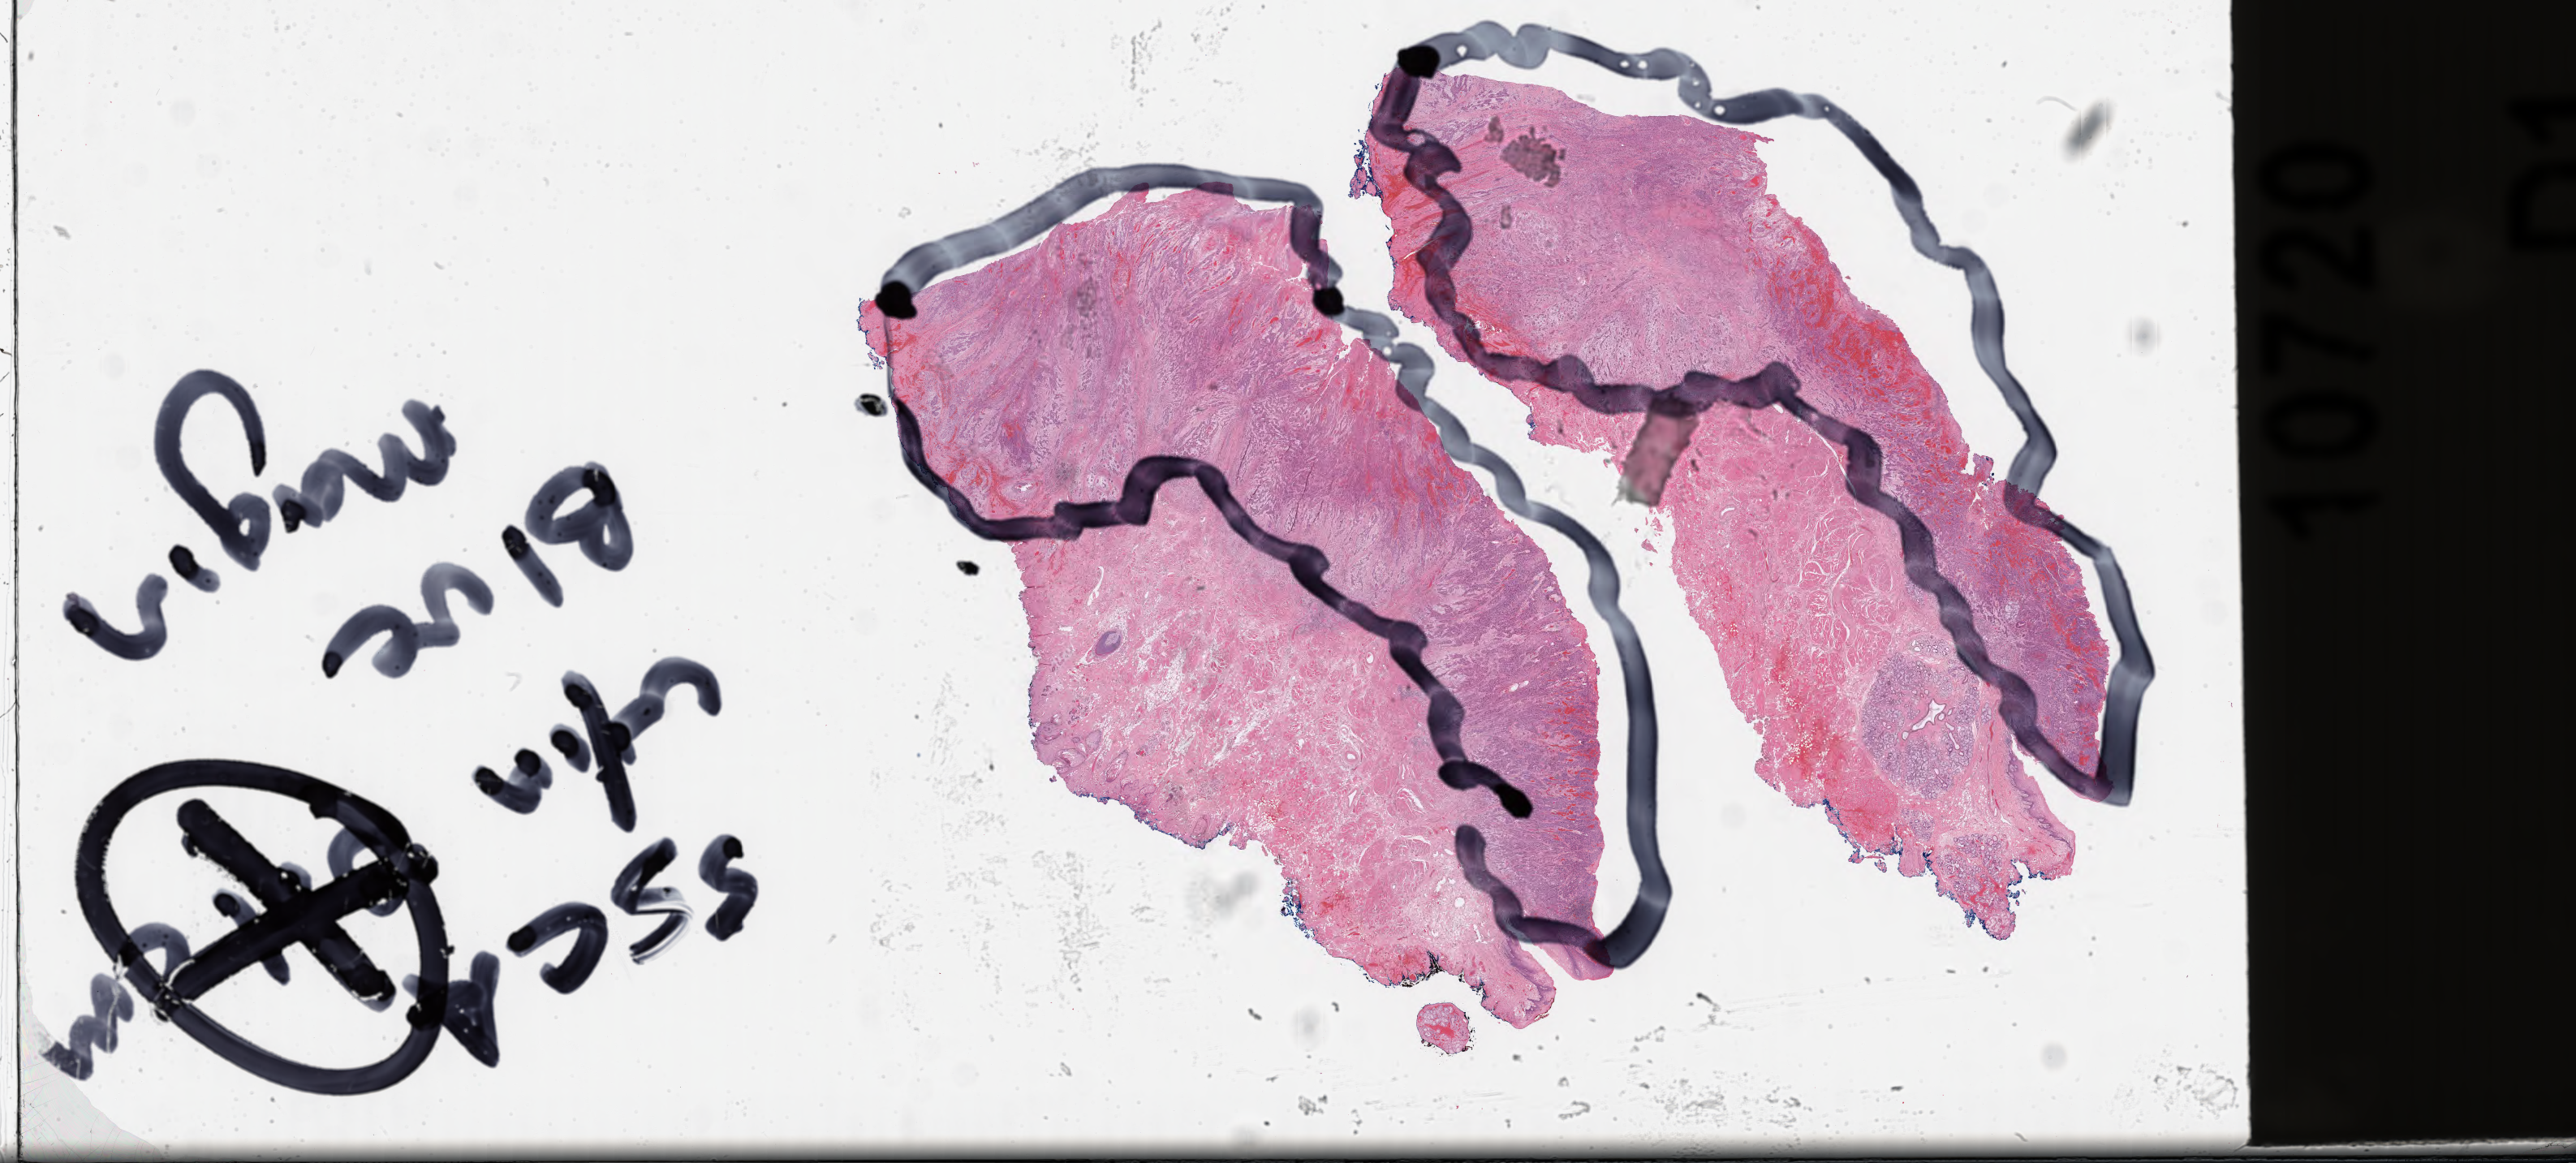
Hematoxylin and eosin (H&E) stained whole-slide image, shown as a low-resolution overview of the whole scanned area (about 50.0 x 22.6 mm). Formalin-fixed paraffin-embedded (FFPE) diagnostic section. Head and neck, primary tumour sample. Male, age 54 years at initial diagnosis.
Histologic diagnosis: Squamous cell carcinoma, NOS.